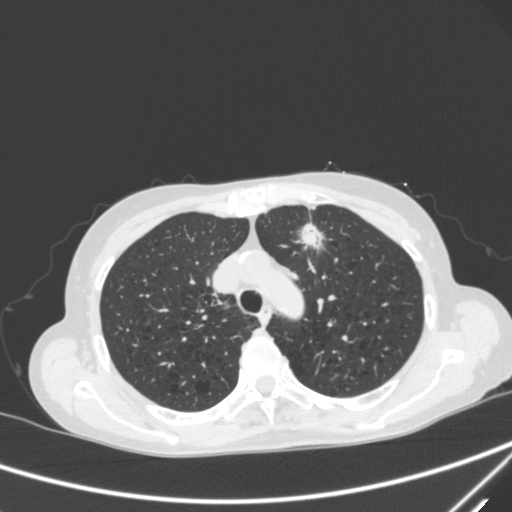
Chest CT, one axial slice; position 227 of 300 along the scan axis; lung window (W 1500 / L -600 HU); 1 mm slice thickness; 512 × 512 image matrix. Female patient, age 71 years. From the clinical record (not read from this slice): clinical TNM (as recorded): T1c N0 M0; histopathological grade: G2-3.
Structures marked on this image (rectangle marked by the reading radiologist):
- lung tumour (recorded histology: adenocarcinoma): bounding box <295,220,334,262> (left, top, right, bottom; pixels)